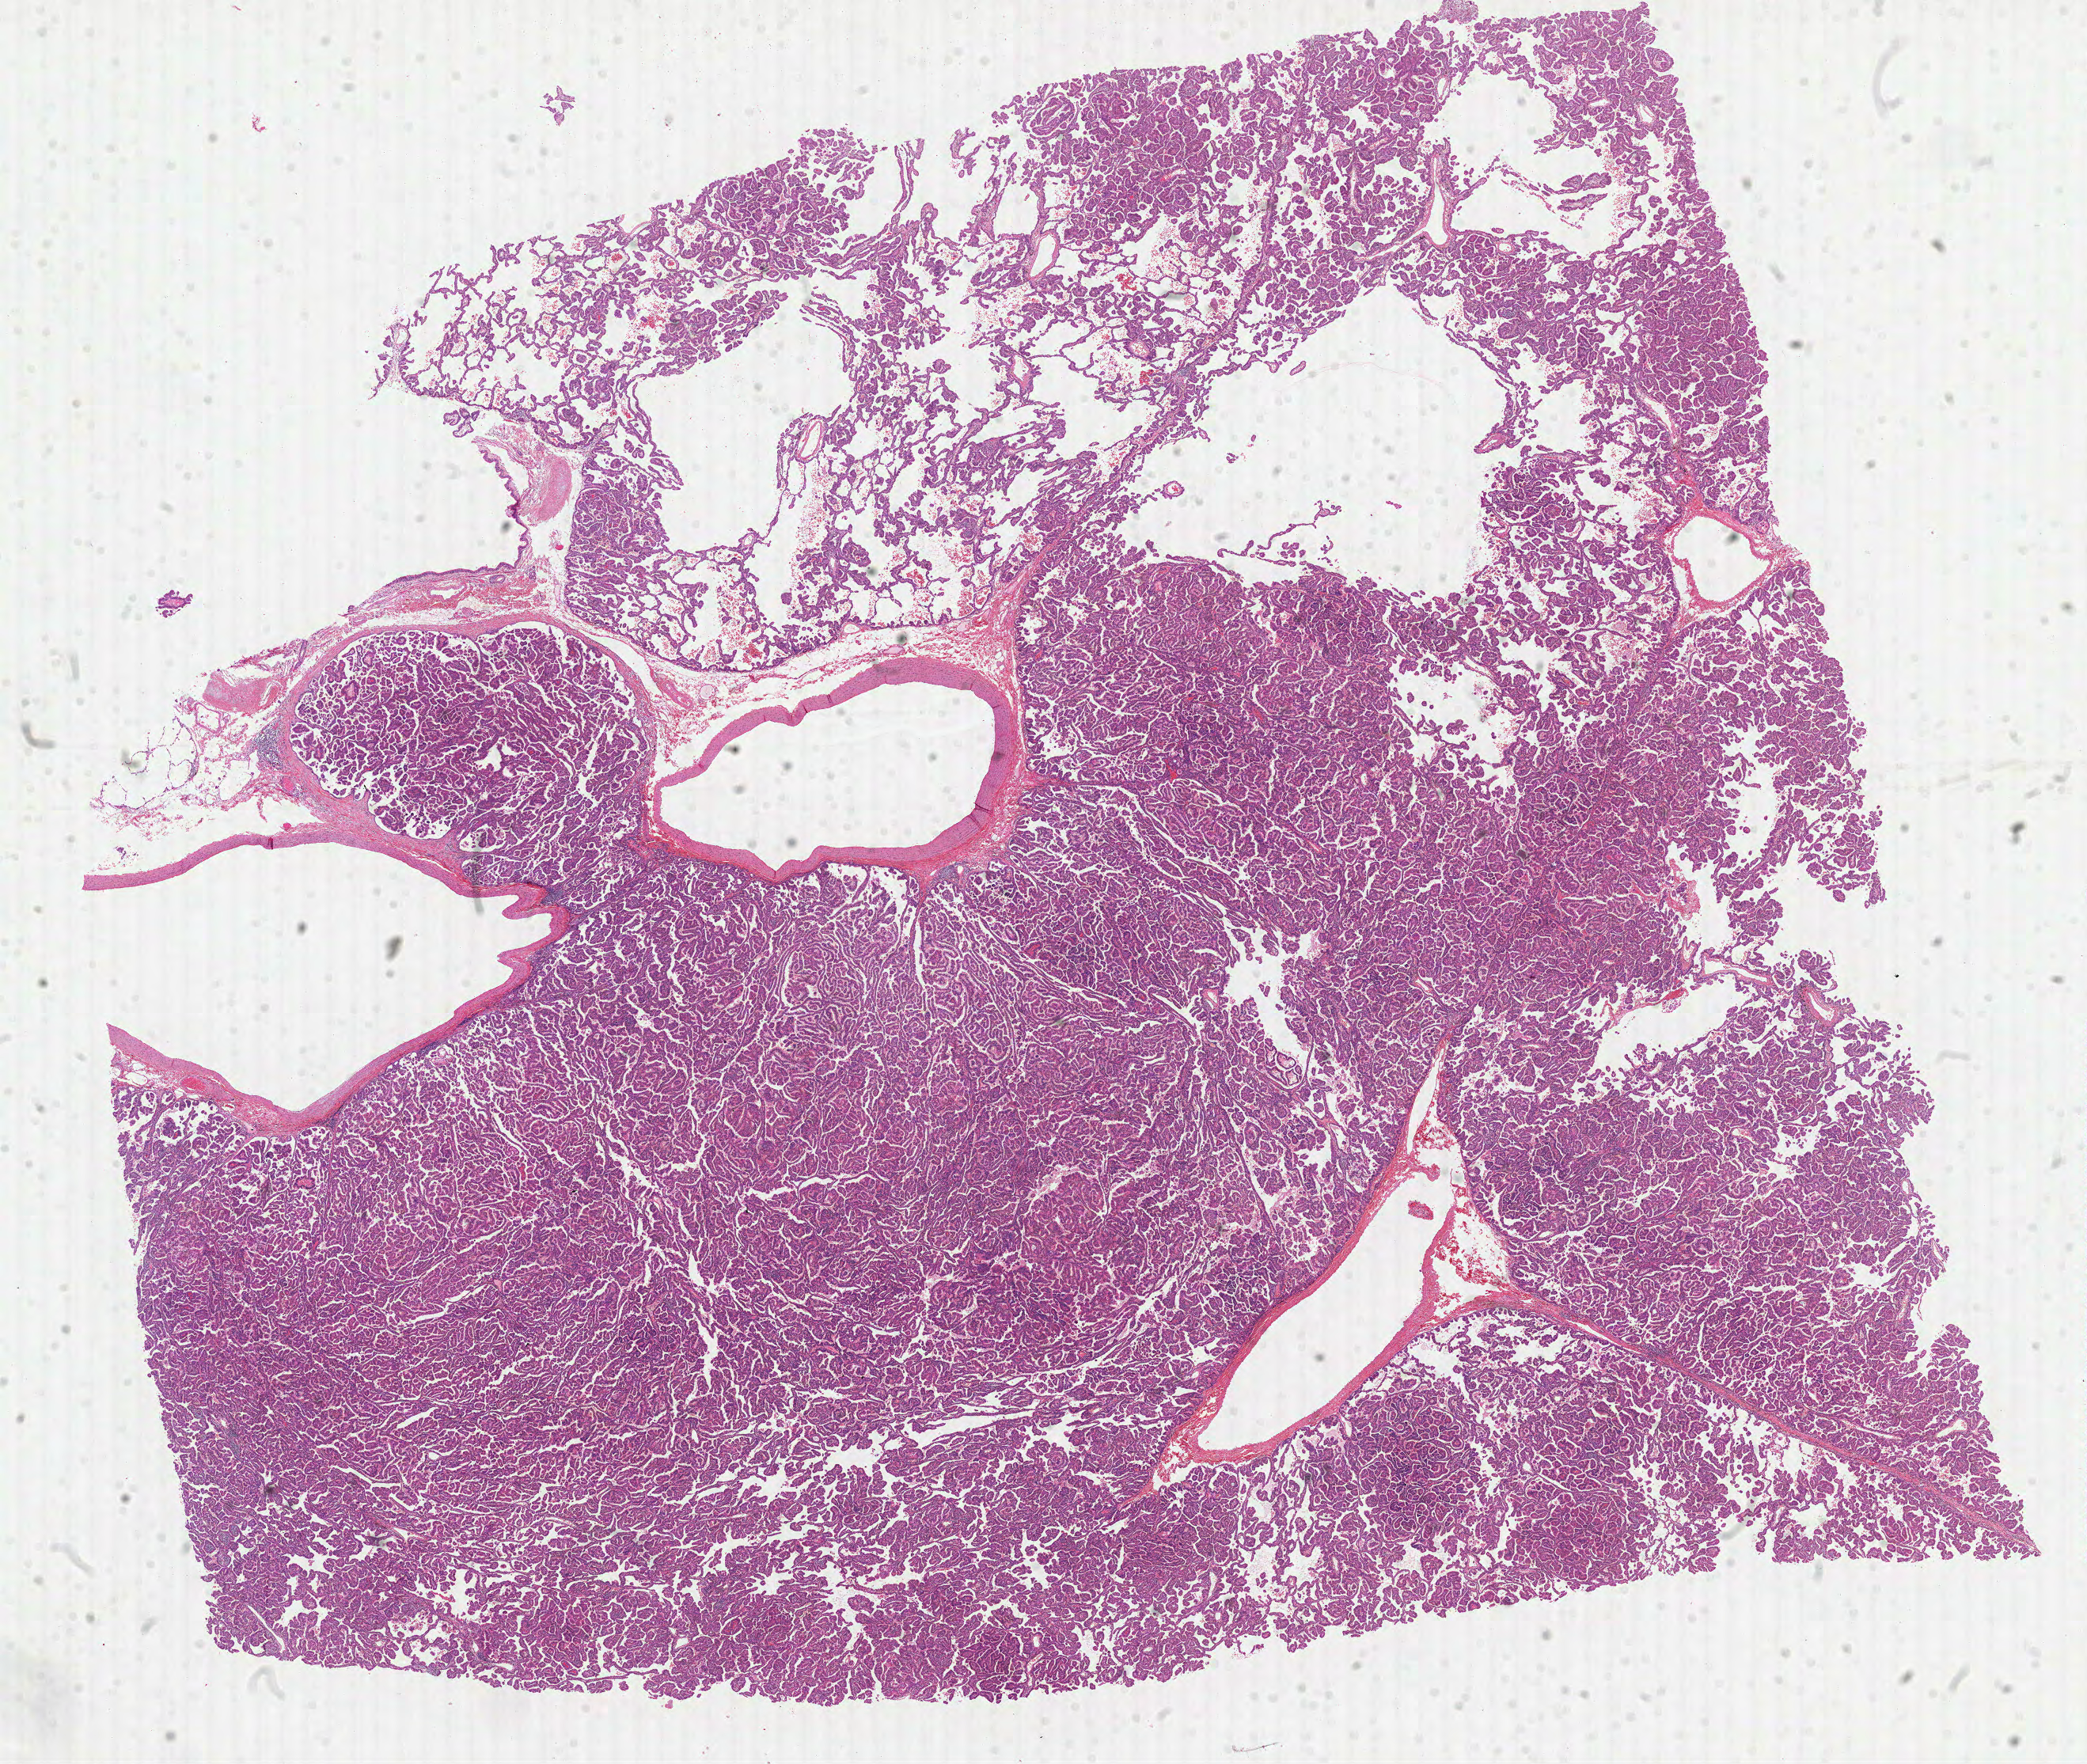
H&E whole-slide image — shown as a low-resolution overview of the whole scanned area (about 21.3 x 18.0 mm); formalin-fixed paraffin-embedded (FFPE) diagnostic section; sample: primary tumour, lung. Patient: male, age at initial diagnosis 62 years.
TNM: T4 N1 M1. AJCC pathologic stage: IV (6th edition). Pathologic diagnosis: Adenocarcinoma with mixed subtypes.